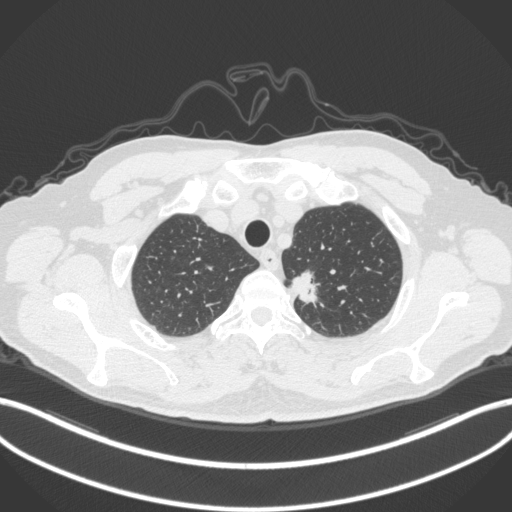
Chest CT, one axial slice; slice 324 of 382 in the series (ordered by position); reconstruction kernel B31f; 120 kVp; lung window (W 1500 / L -600 HU); 1 mm slice thickness; 512 × 512 image matrix, field of view 400 × 400 mm. Patient: male, 64 years. From the clinical record (not read from this slice): clinical TNM (as recorded): T1c N0 M0.
Annotated regions visible in this slice (bounding box drawn by a radiologist):
- lung tumour (recorded histology: adenocarcinoma): bounding box <287,262,325,314> (left, top, right, bottom; pixels)